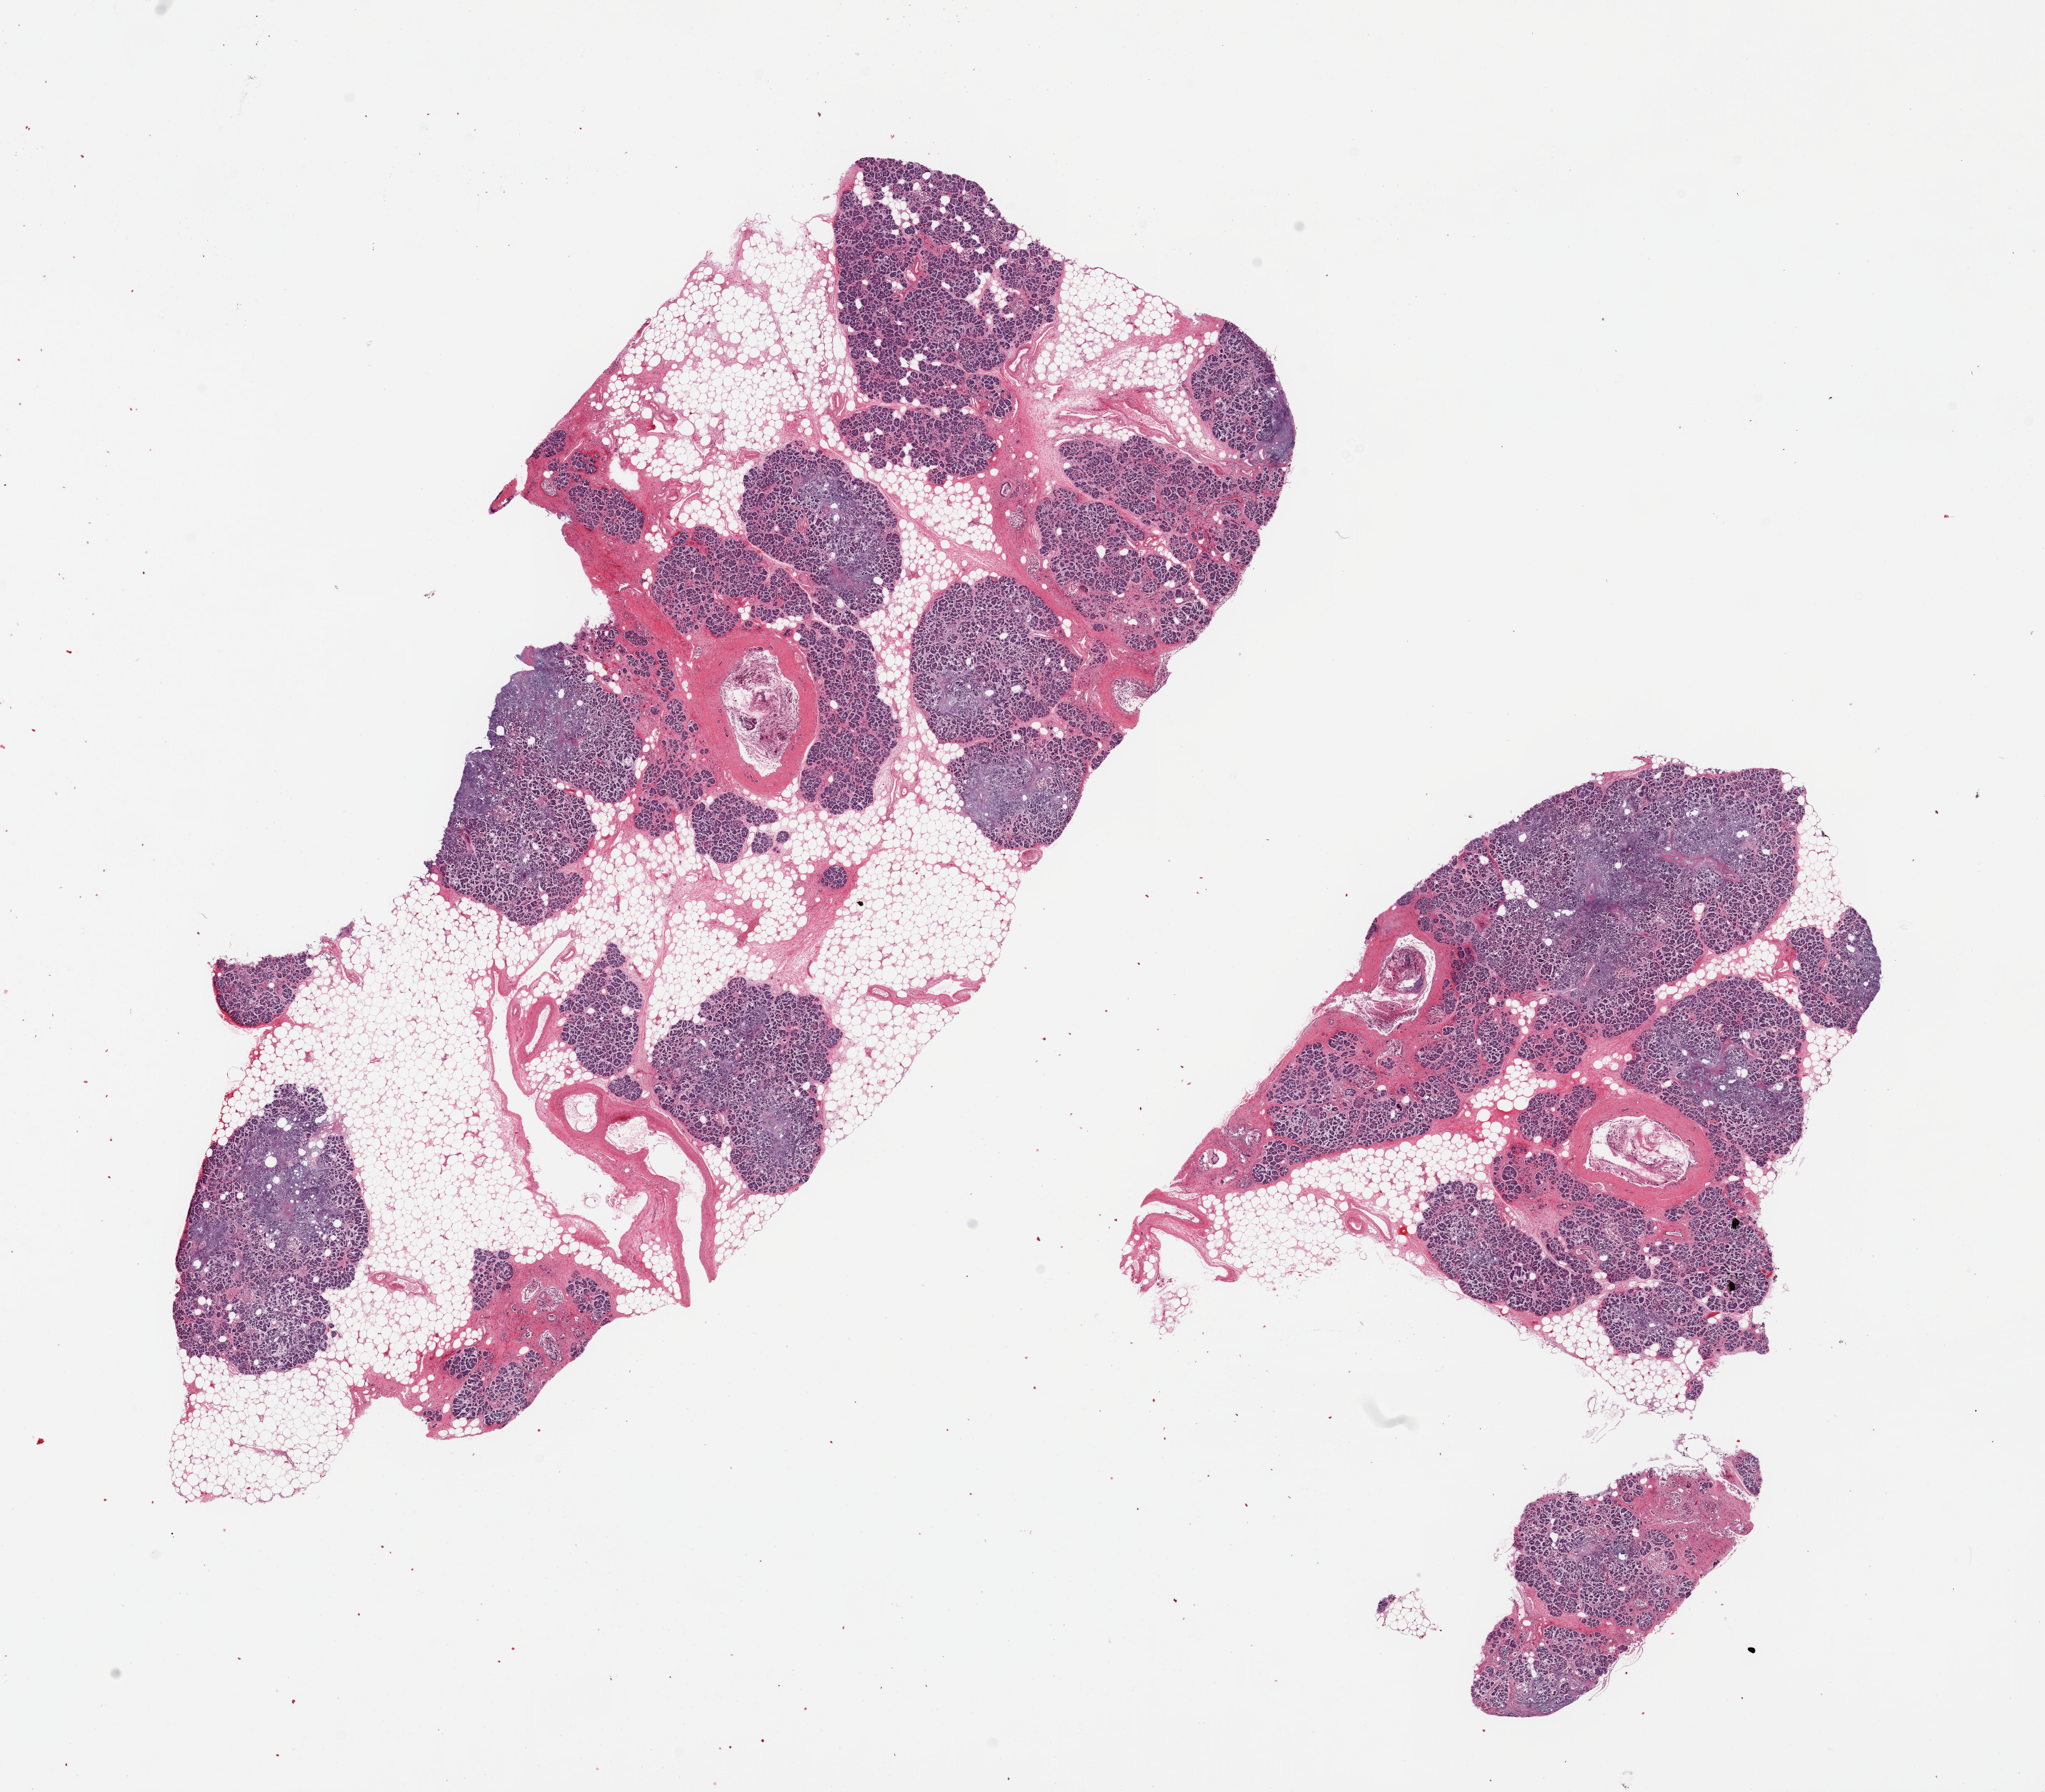
Digitized haematoxylin and eosin-stained section, brightfield — shown as a low-resolution overview of the whole scanned area (about 22.6 x 19.8 mm, slide scanned at 20x). PAXgene-fixed, paraffin-embedded tissue. Target tissue: pancreas. Tissue donor sample. Donor sex: male.
Reviewer comment on this tissue sample: 2 pieces modeate-severe autolysis, saponification.